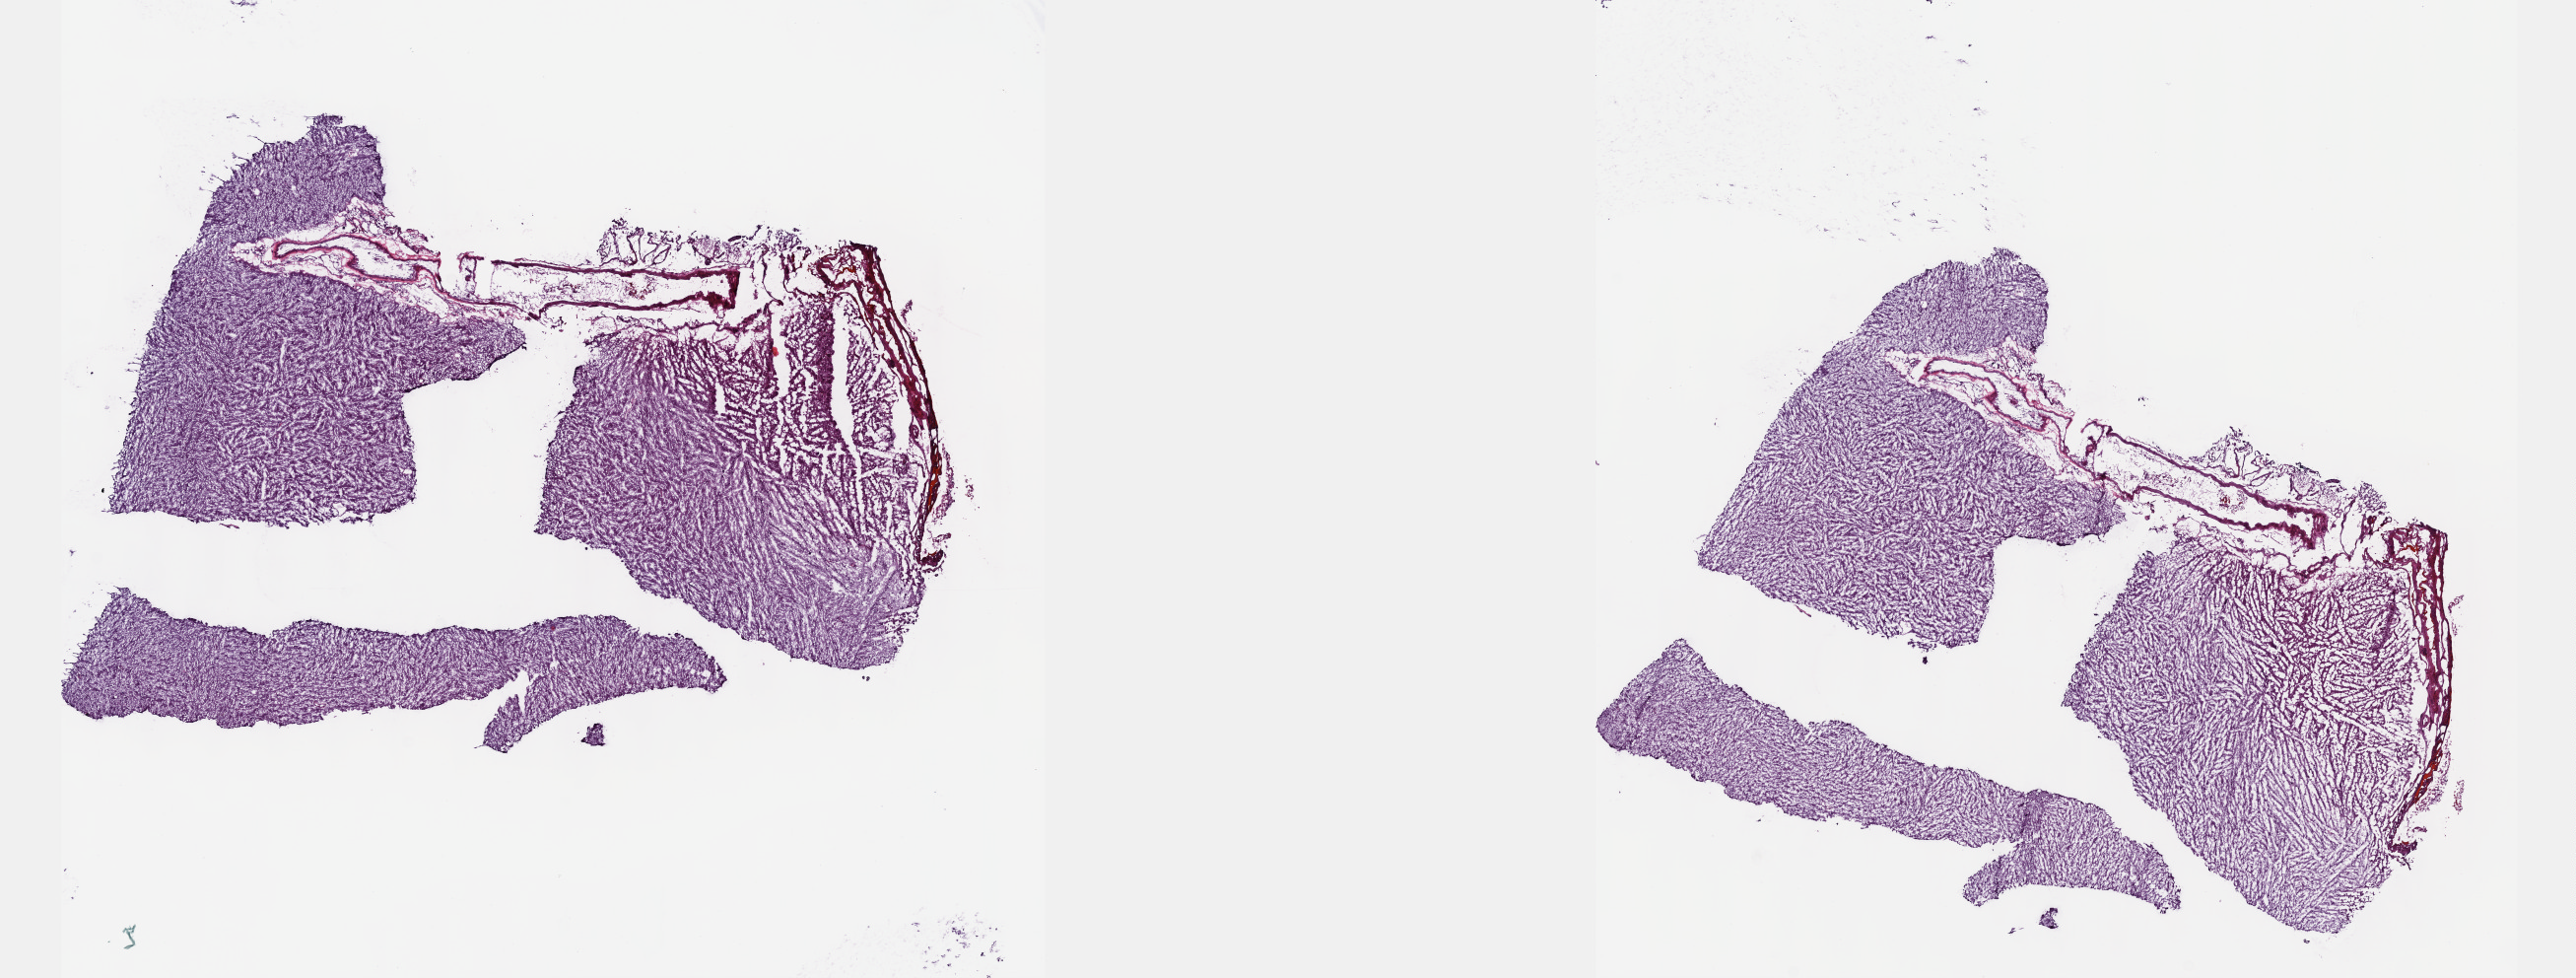
Hematoxylin and eosin (H&E) stained whole-slide image — a low-resolution overview of the entire scanned area, about 21.1 x 8.0 mm, frozen section from the top of the tissue portion, primary tumour sample from the brain. Patient: female, age at initial diagnosis 27 years.
Histologic diagnosis: Oligodendroglioma, NOS (cerebrum).